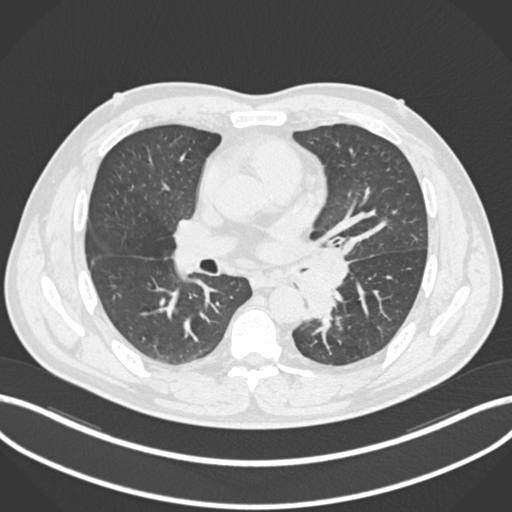
Chest CT, one axial slice. Position 121 of 223 along the scan axis. Reconstruction kernel B30f. Lung window (W 1500 / L -600 HU). 1 mm slice thickness. 512 × 512 image matrix. Male patient, age 50 years. From the clinical record (not read from this slice): clinical TNM (as recorded): T2a N3 M0.
Structures marked on this image (rectangle marked by the reading radiologist):
- lung tumour (recorded histology: squamous cell carcinoma): bounding box <296,250,355,320> (left, top, right, bottom; pixels)